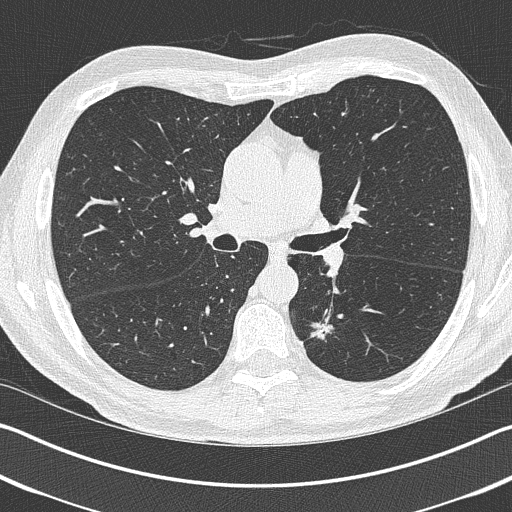
Low-dose screening chest CT, one axial slice. Slice 244 of 402 in the series (ordered by position). Reconstruction kernel B50f. Lung window (W 1500 / L -600 HU). 1 mm slice thickness. 512 × 512 image matrix, field of view 340 × 340 mm.
Annotated regions visible in this slice (expert manual segmentation):
- lesion 1 (tumor, lower lobe of left lung): bounding box [x1, y1, x2, y2] px = [311, 323, 334, 340]